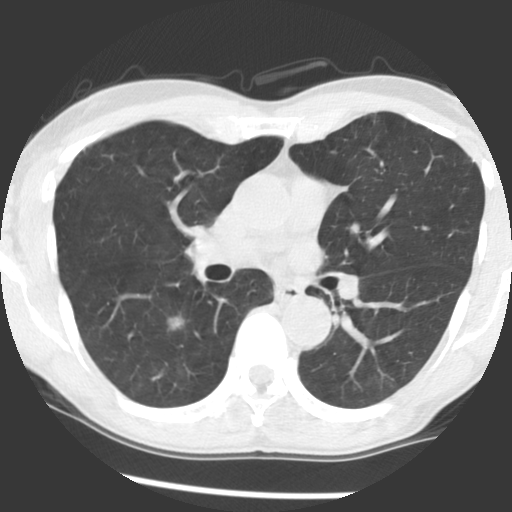
Low-dose screening chest CT, axial slice; baseline screening round; lung window (W 1500 / L -600 HU); 2.5 mm slice thickness; slice 97 of 165 in the series. Male participant, aged 65 years at enrolment. Current smoker at enrolment.
• Expert-annotated lung lesion, bounding box [x1, y1, x2, y2] px = [144, 296, 205, 344].
• The screening reader recorded 2 non-calcified nodules or masses ≥4 mm on this exam; which of them this box marks is not recorded.